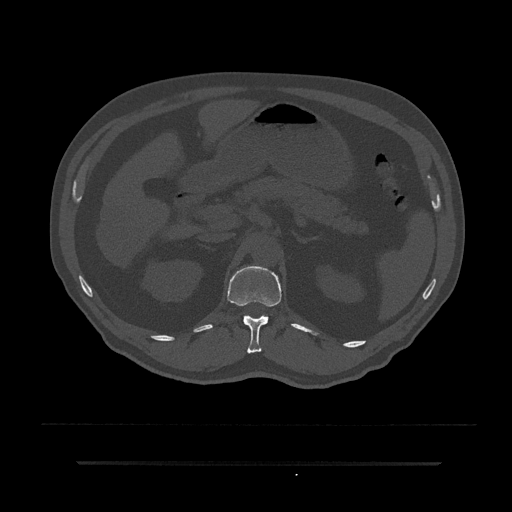
CT including the spine, one axial slice. Reconstruction kernel Br40s/3. Bone window (W 1800 / L 400 HU). 0.5 mm slice thickness. 512 × 512 image matrix, field of view 464 × 464 mm. Patient: male, 59 years. Case-level facts recorded for this patient, not image findings: primary cancer: bile ducts.
Annotated regions visible in this slice (semi-automatic segmentation, software-assisted and operator-edited):
- T12 vertebra: box from (x=227, y=266) to (x=282, y=354) px